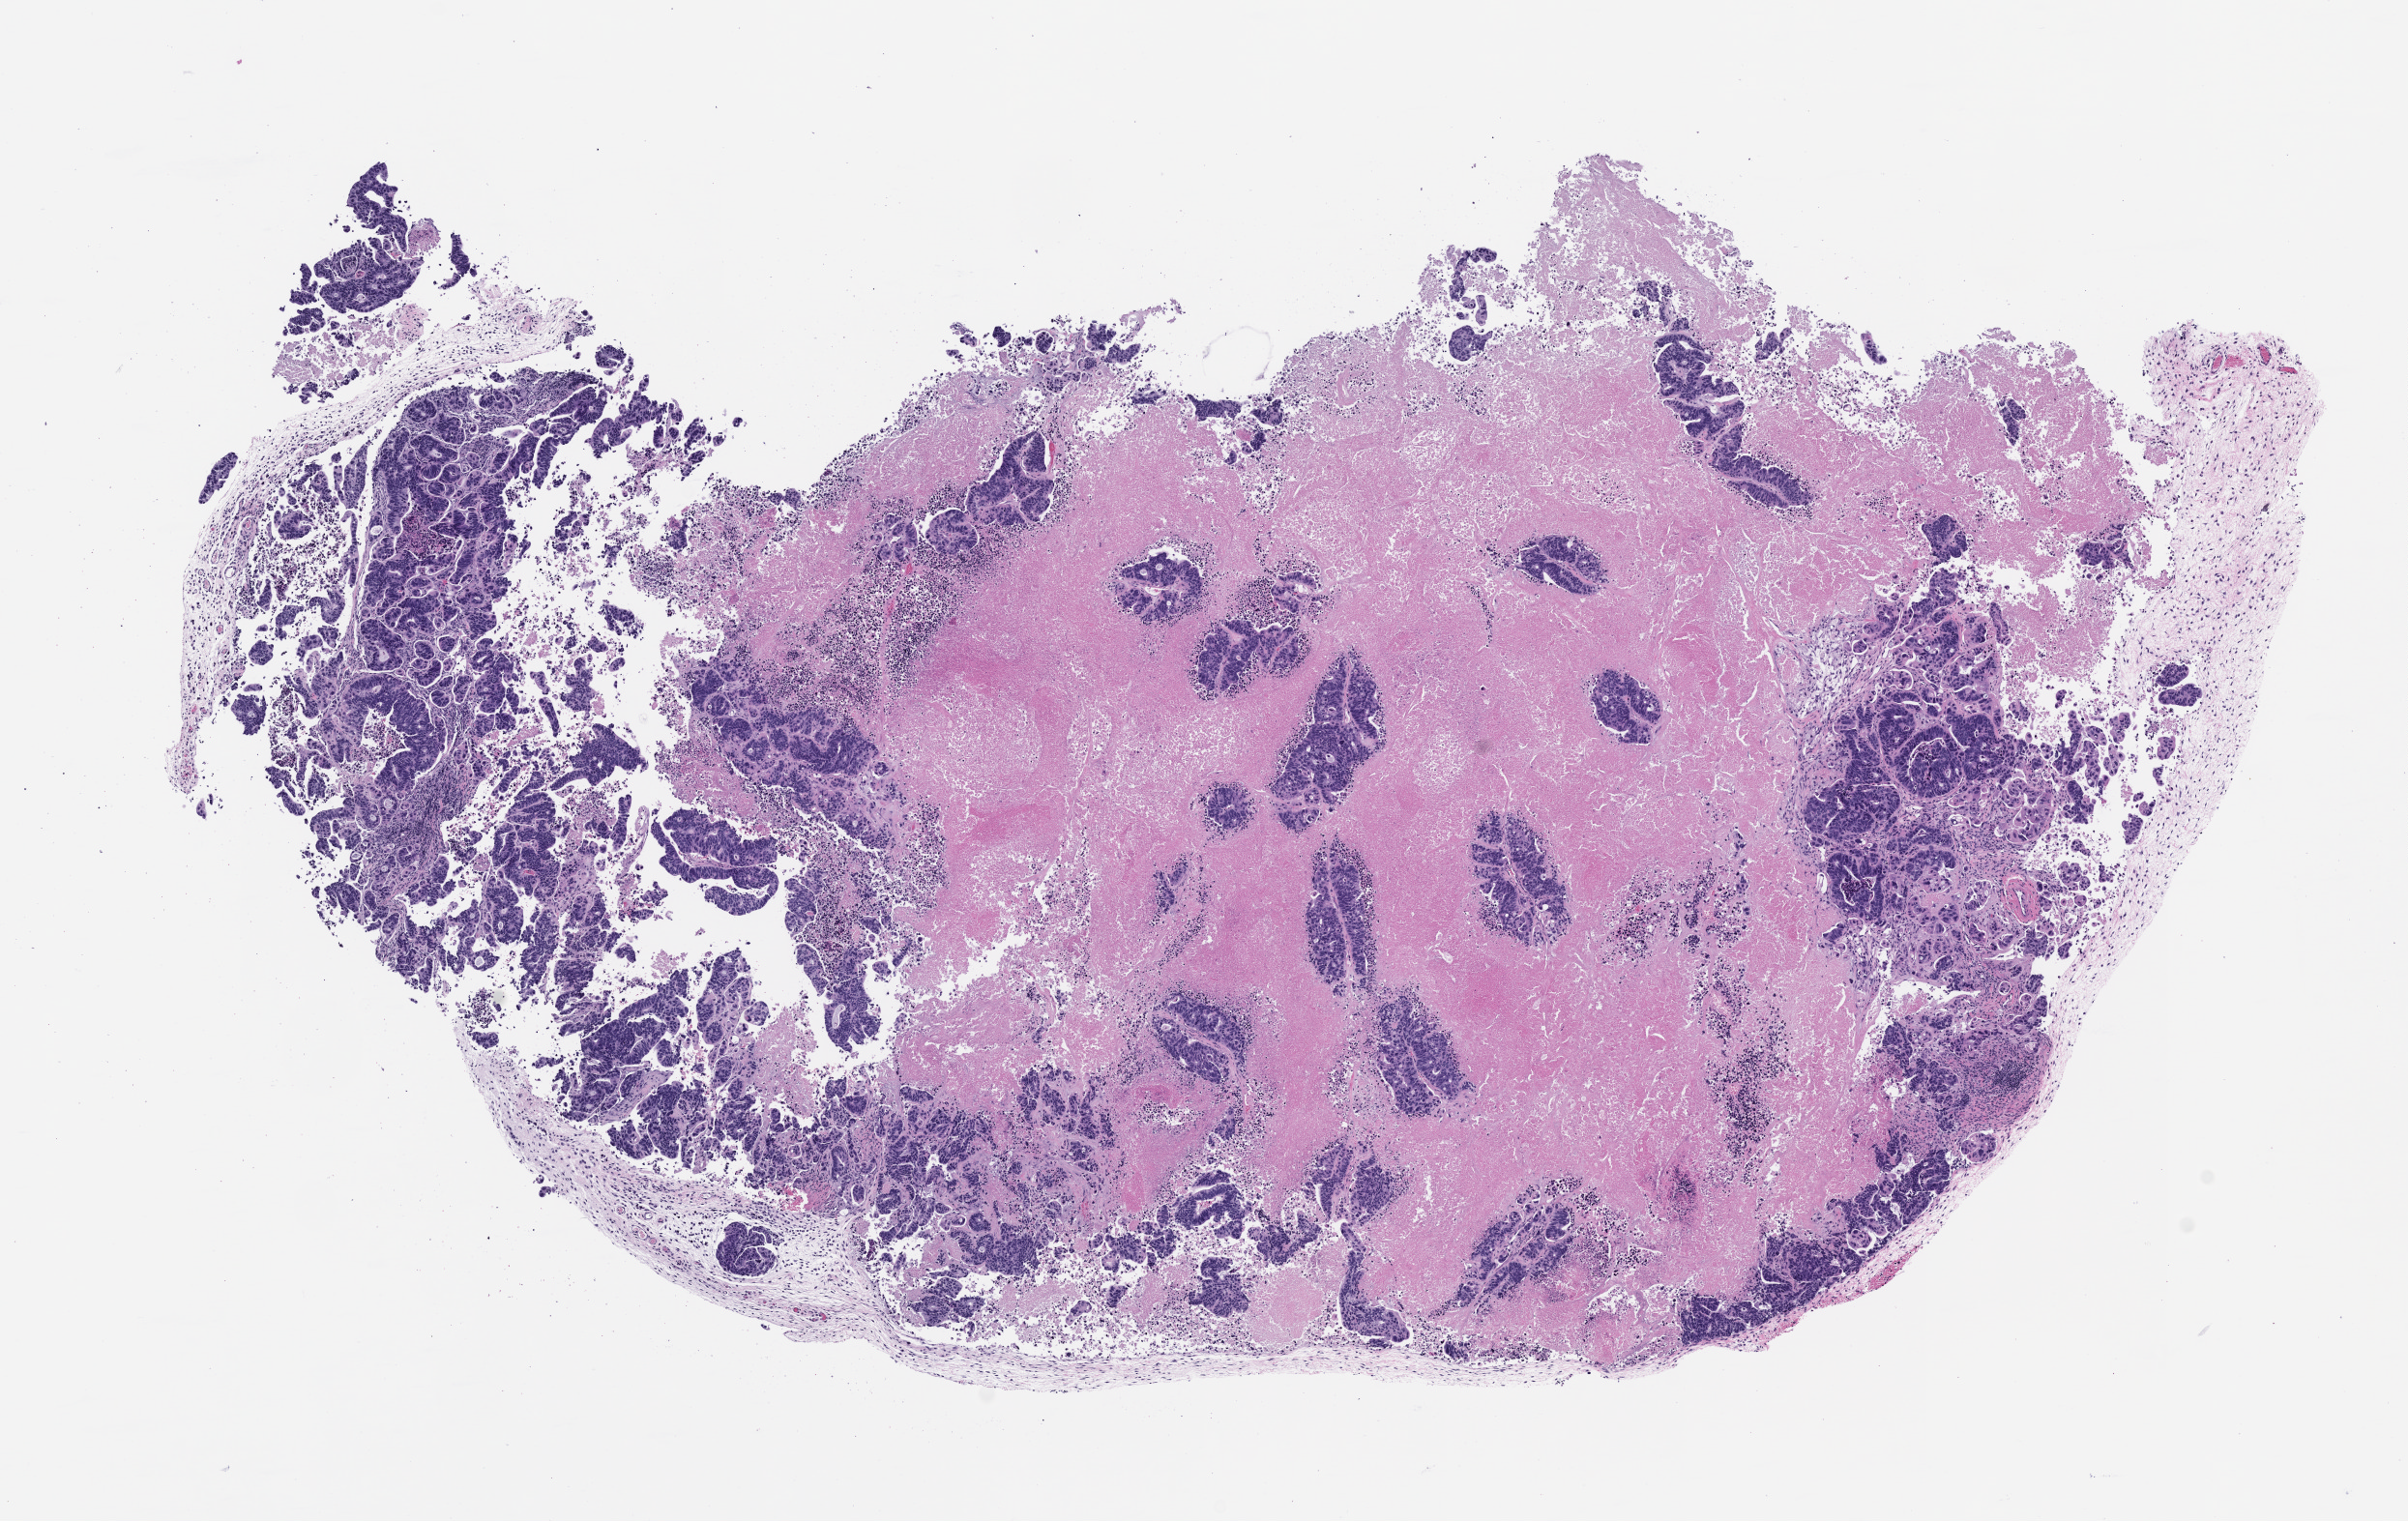
Whole-slide image, H&E: patient-derived xenograft (human tumor grown in a mouse), passage 1 — whole scanned area (about 10.0 x 6.3 mm) shown as a low-resolution overview. Formalin-fixed paraffin-embedded section. Tumor site category: colon.
Originating patient diagnosis: Colon Adenocarcinoma.